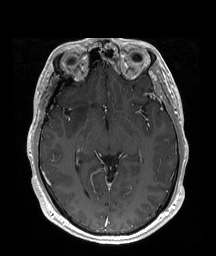
Brain MRI from a brain-tumour surgery series, one axial slice; slice 111 of 192 in the series (ordered by position); T1-weighted post-contrast; 1 mm slice thickness; 216 × 256 image matrix, field of view 219 × 260 mm. Case-level facts recorded for this patient, not image findings: histopathology: Astrocytoma; WHO grade: 2; IDH mutation: yes.
Structures marked on this image (expert manual segmentation):
- tumour: bounding box (x1, y1, x2, y2) in pixels: (68, 96, 91, 135)